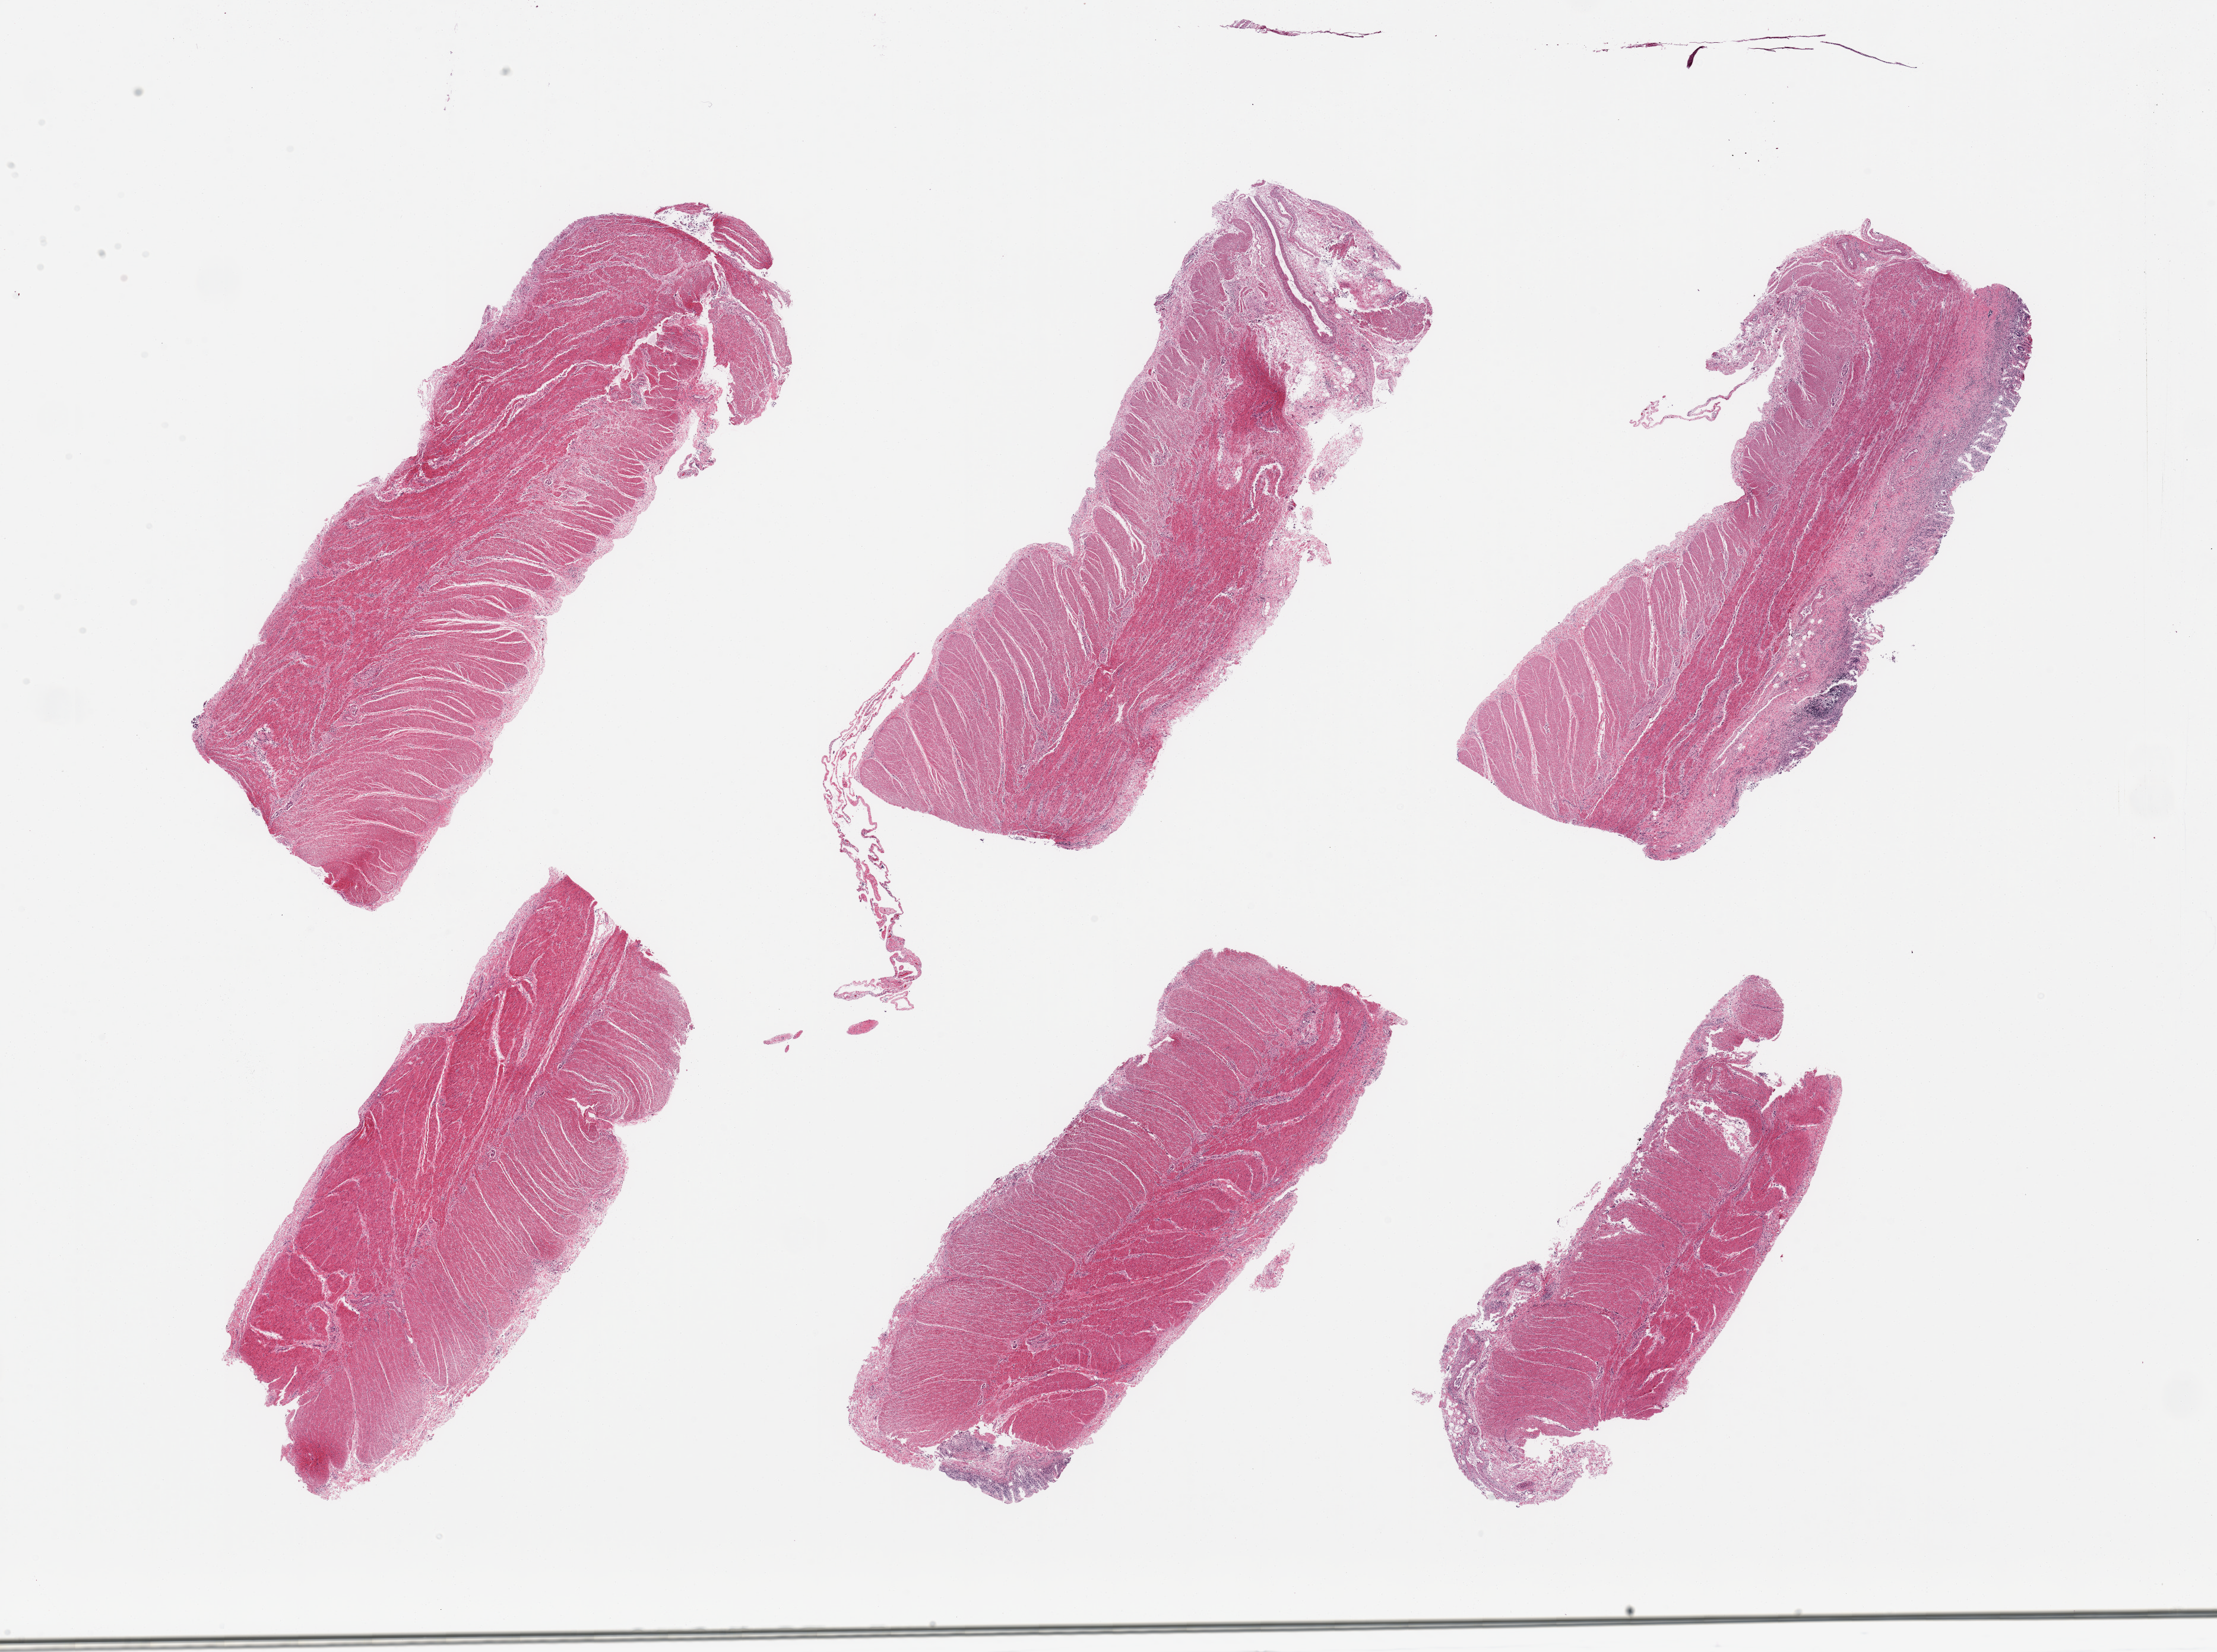
Whole-slide image, haematoxylin and eosin stain, whole scanned area (about 29.5 x 22.0 mm, slide scanned at 20x) shown as a low-resolution overview, PAXgene-fixed paraffin-embedded (PFPE) section, sampled site (target tissue): sigmoid colon, tissue donor sample. Donor: female.
Review note (as recorded): 6 pieces, confirmed target muscularis; trace 'contaminant' autolyzed mucosa.